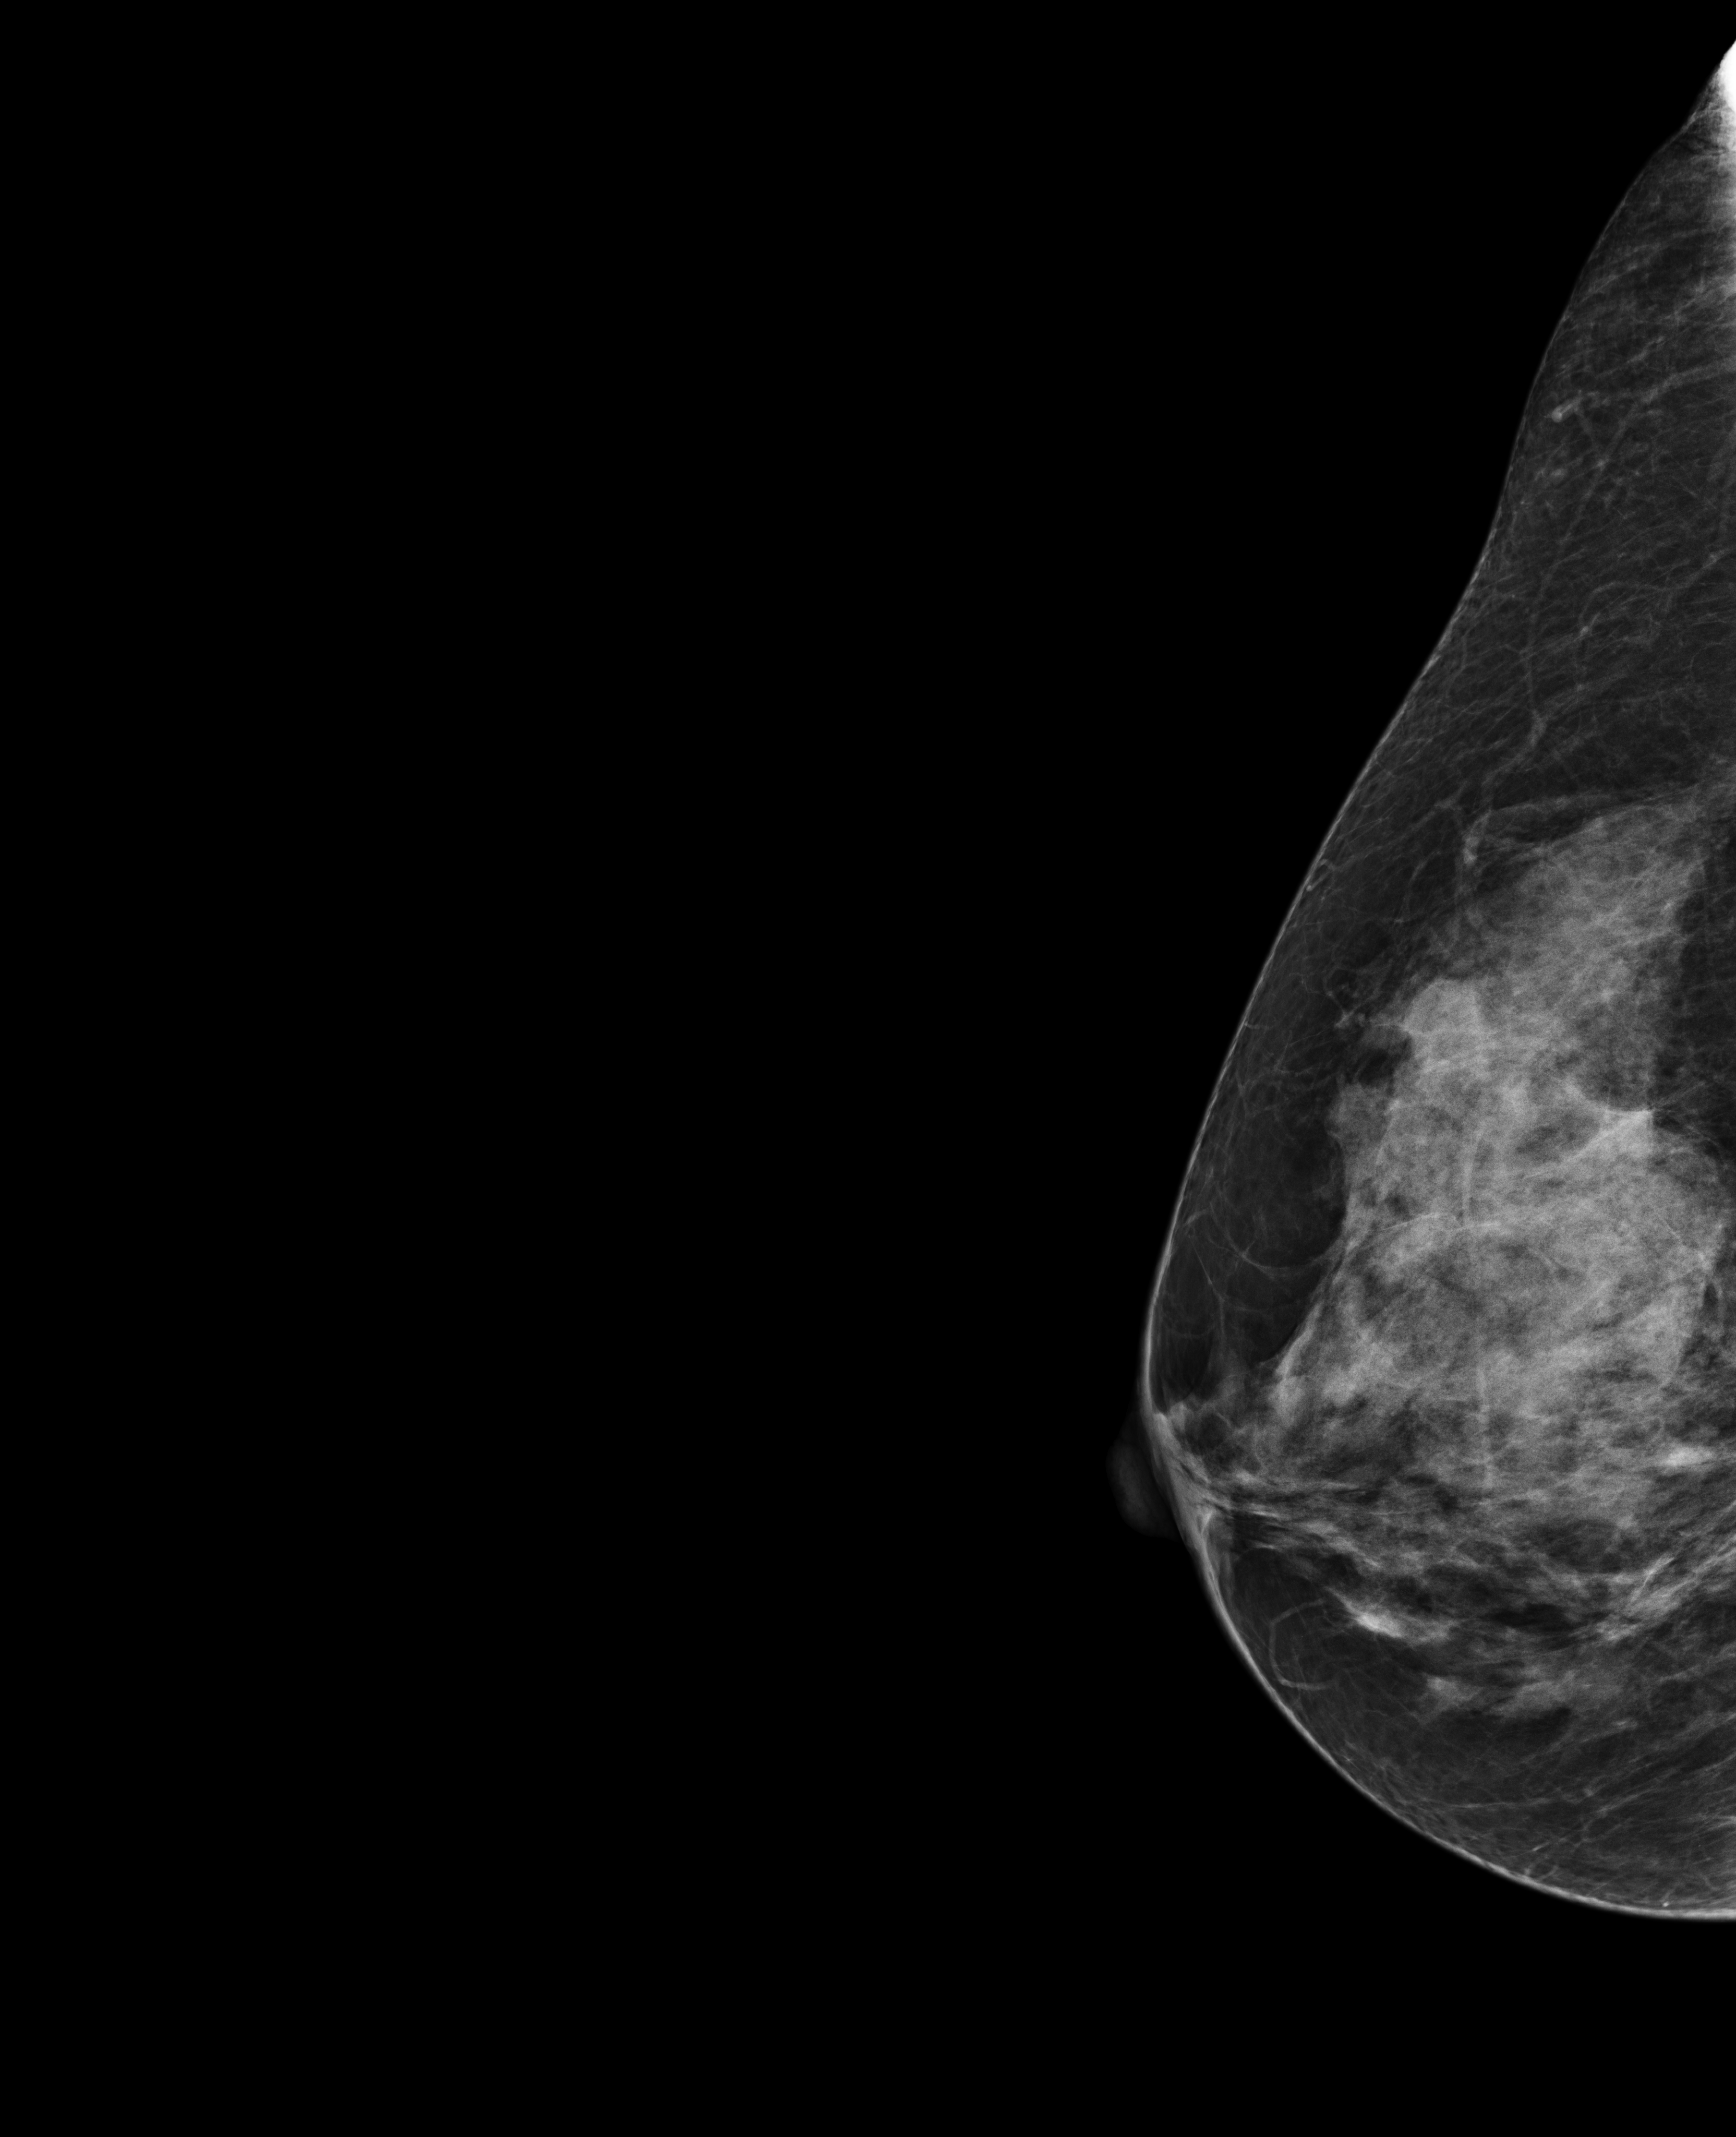
Full-field digital mammogram (FFDM); right breast; exaggerated CC view (lateral); annual screening mammography examination; system: Selenia Dimensions. Female patient, age 50 years.
- breast density at the screening exam (both breasts): extremely dense (BI-RADS density category d)
- final BI-RADS category for the screening round (tomosynthesis exam, both breasts): category 1
- recall: no recall after this screen